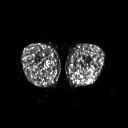
FDG PET of an extremity soft-tissue mass (from a PET/CT study), one axial slice; position 211 of 267 along the scan axis; 128 × 128 image matrix, field of view 500 × 500 mm. Patient: male, 27 years. From the clinical record (not read from this slice): histological type: extraskeletal osteosarcoma; grade: high; site of the primary tumour: left adductur.
Structures marked on this image (expert contour drawn on MRI and transferred to this co-registered scan by the dataset authors):
- gross tumour volume (mass): bounding box <82,64,87,67> (left, top, right, bottom; pixels)